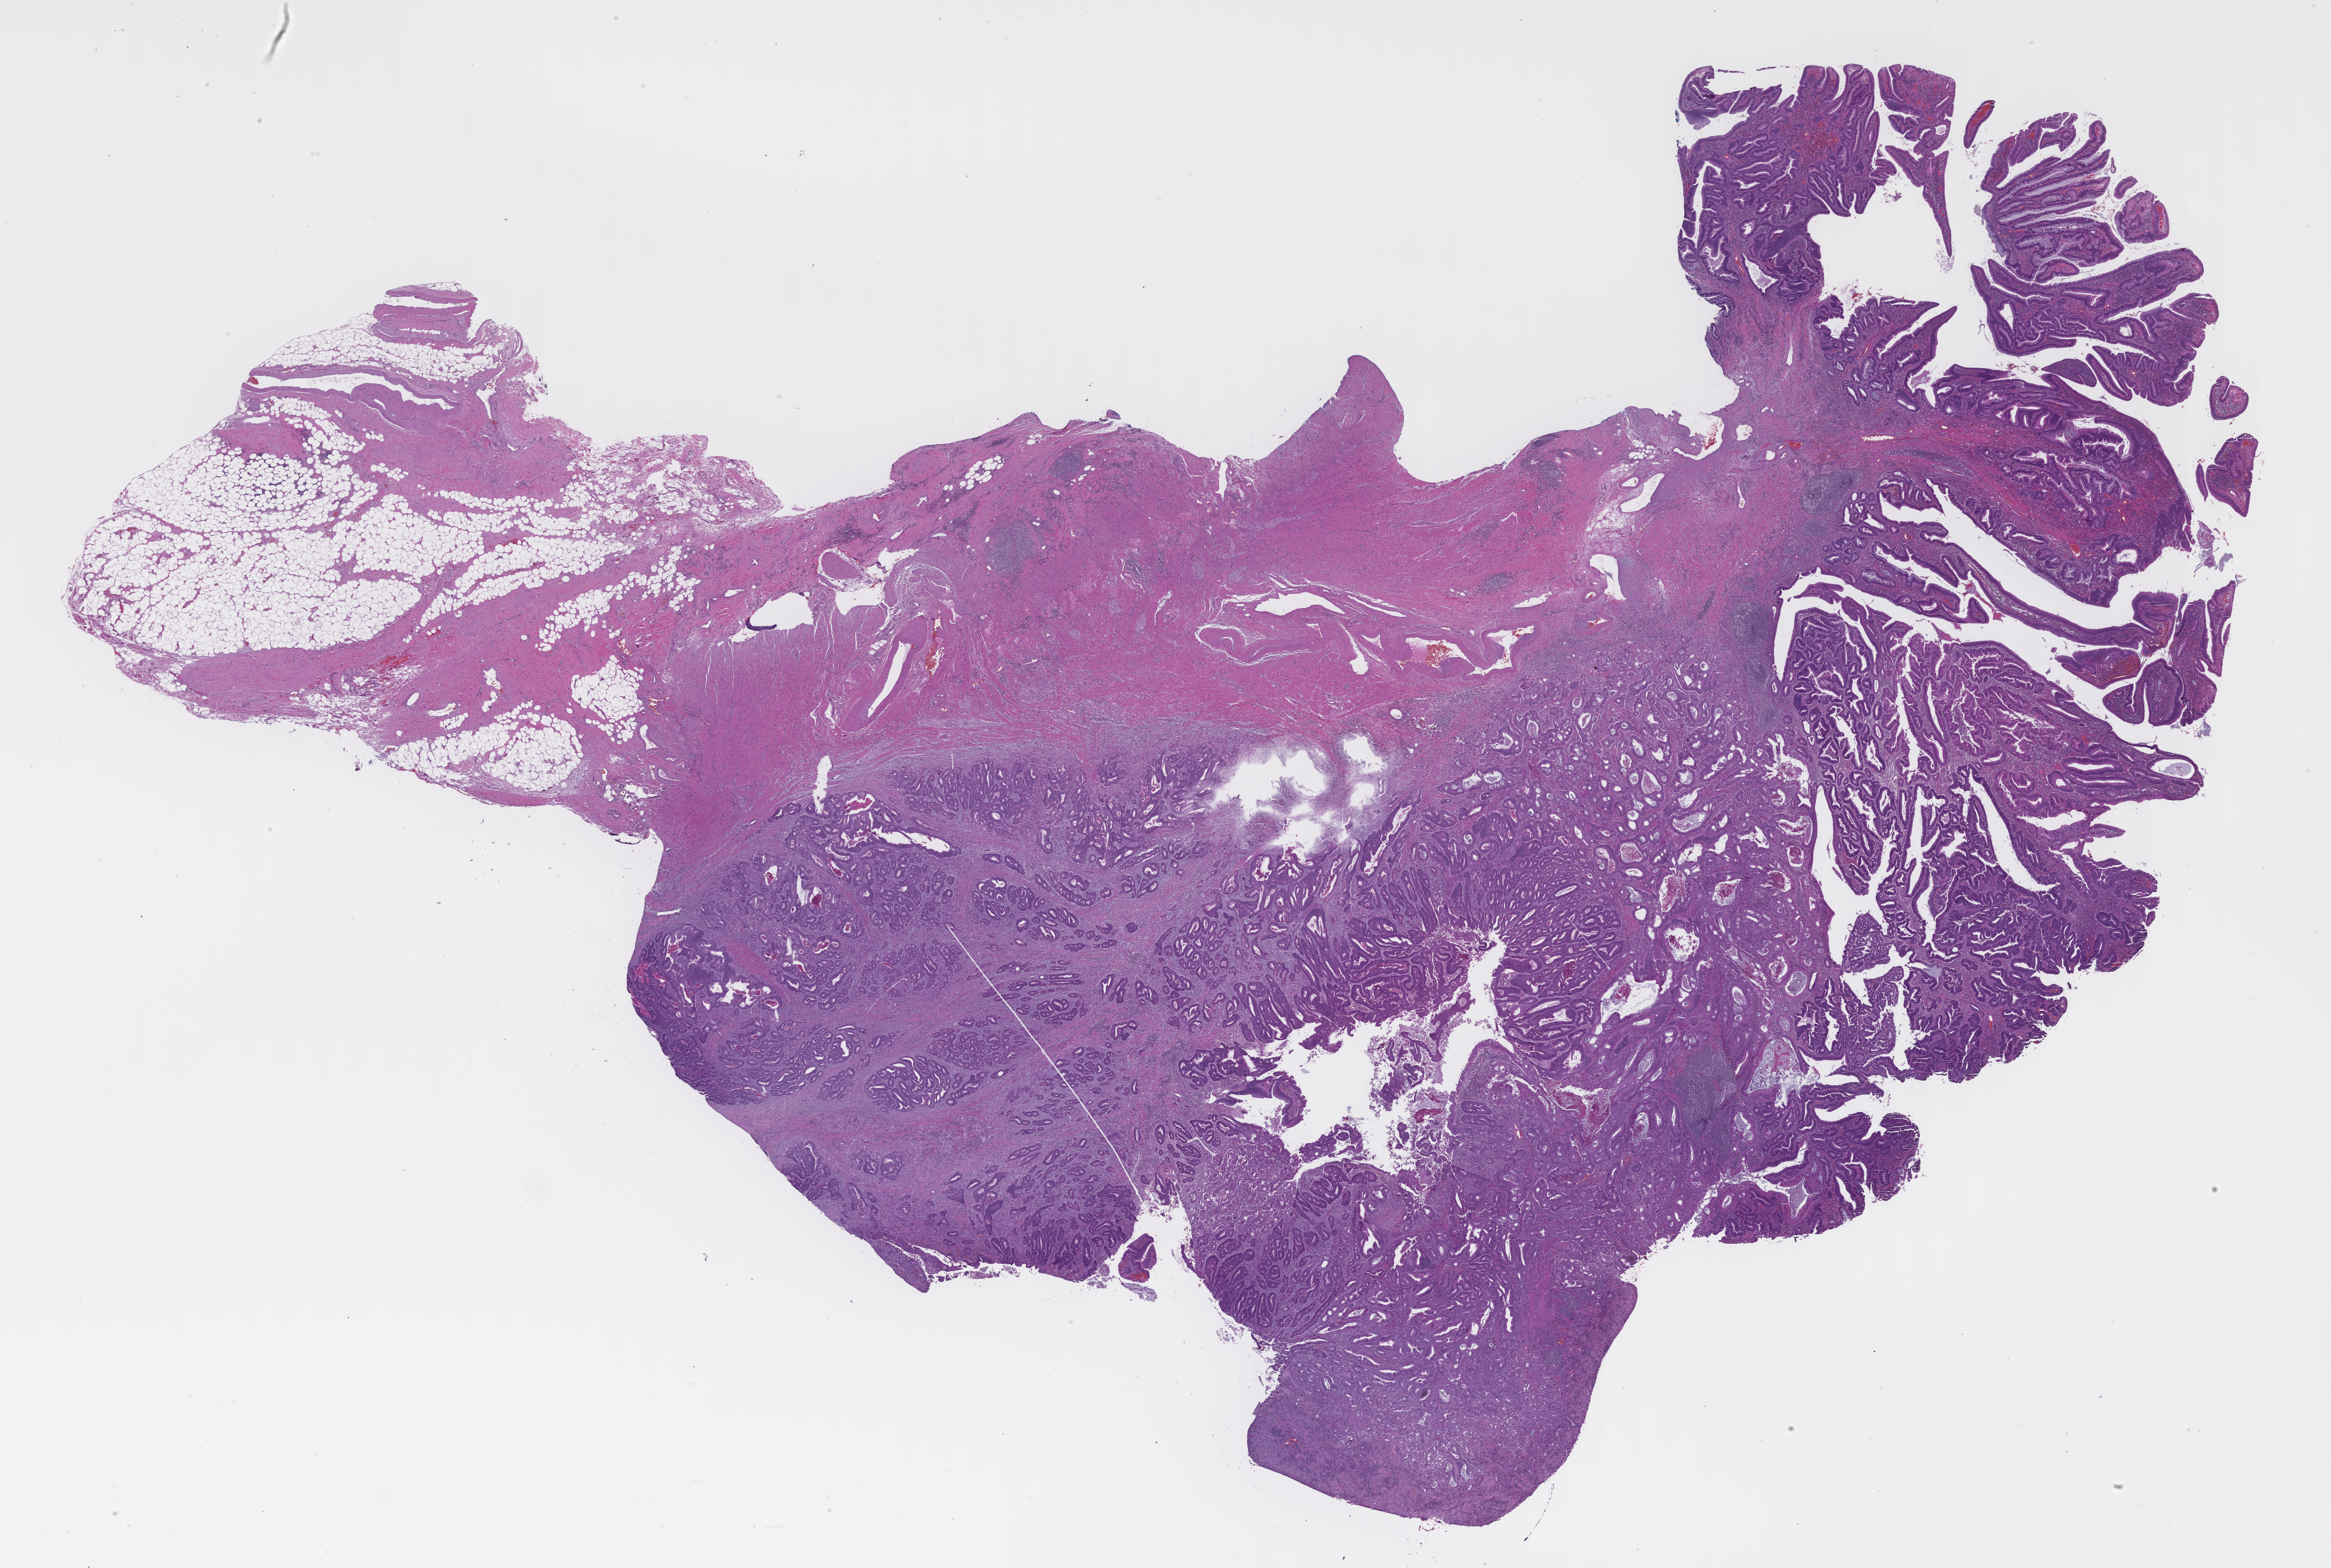
Digitized haematoxylin and eosin-stained section, a low-resolution overview of the entire scanned area, about 32.2 x 21.6 mm; FFPE section; site: colon; specimen time point: archival tissue. Patient sex: male.
* this section: primary tumour tissue
* diagnosis: Colorectal Carcinoma